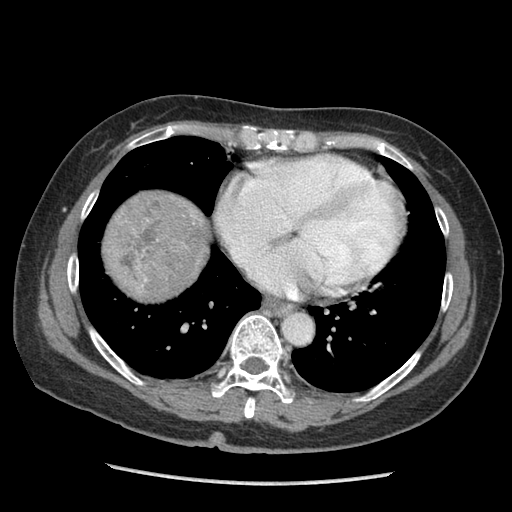
Contrast-enhanced abdominal CT (liver protocol), one axial slice. Slice 94 of 105 in the series (ordered by position). 140 kVp. Soft-tissue window (W 400 / L 40 HU). 2.5 mm slice thickness. 512 × 512 image matrix. From the clinical record (not read from this slice): diagnosis: hepatocellular carcinoma (patient treated with transarterial chemoembolisation; whether this scan precedes or follows treatment is not stated here); TNM stage (as recorded): Stage-I; Child-Pugh class: A; tumour differentiation: moderately differentiated.
Annotated regions visible in this slice (semi-automatic segmentation, software-assisted and operator-edited):
- liver parenchyma outside the tumour (the mass and vessels are separate outlines, so this box may not span the whole liver): bounding box [x1, y1, x2, y2] px = [102, 200, 127, 253]
- mass: [102, 189, 212, 304]